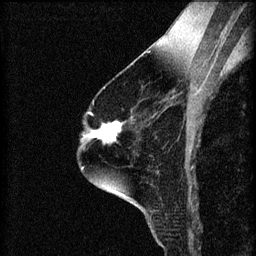
Breast MRI (dynamic contrast-enhanced), one sagittal slice; slice 42 of 60 in the series (ordered by position); 3 images stored at this slice position (order not interpretable as contrast timing); 1.5 T; TE 4.2 ms, TR 8.2 ms; 2 mm slice thickness; 256 × 256 image matrix, field of view 180 × 180 mm. Patient: female, 60 years.
Structures marked on this image (semi-automatic segmentation, software-assisted and operator-edited):
- analysis volume of interest (the breast-tissue region the enhancement analysis was run in; not a lesion): bounding box (x1, y1, x2, y2) in pixels: (89, 122, 124, 145)
- tumour enhancement mask (voxels above the 70 % enhancement threshold inside the analysis volume of interest): (91, 122, 123, 145)